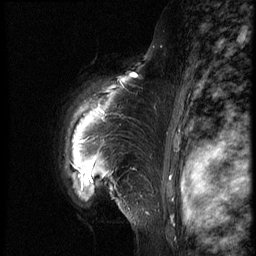
Breast MRI (dynamic contrast-enhanced), one sagittal slice. Slice 54 of 66 in the series (ordered by position). Dynamic contrast-enhanced series, image 2 of 3 at this slice position (ordered by acquisition). 1.5 T. TE 4.2 ms, TR 8.9 ms. 2.5 mm slice thickness. 256 × 256 image matrix, field of view 200 × 200 mm. Female patient, age 39 years. From the clinical record (not read from this slice): setting: breast cancer imaged before/during neoadjuvant chemotherapy; receptor status: HER2-positive.
Annotated regions visible in this slice (semi-automatically segmented with operator editing):
- analysis volume of interest (the breast-tissue region the enhancement analysis was run in; not a lesion): box from (x=53, y=75) to (x=165, y=218) px
- tumour enhancement mask (voxels above the 140 % enhancement threshold inside the analysis volume of interest): (x=89, y=75)–(x=138, y=173)